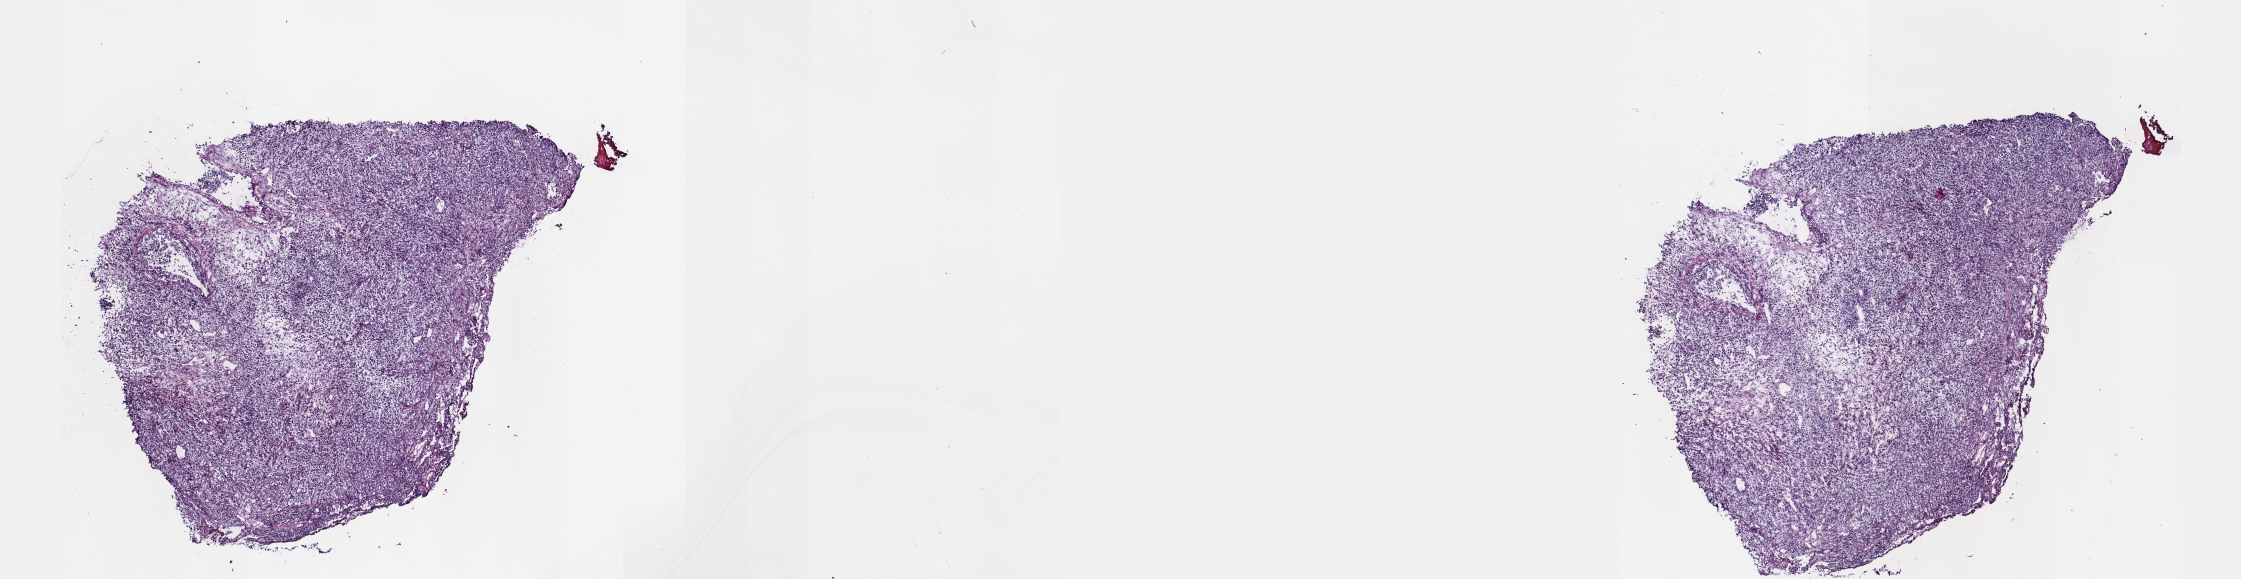
Hematoxylin and eosin (H&E) stained whole-slide image, a low-resolution overview of the entire scanned area, about 18.1 x 4.7 mm, frozen section from the top of the tissue portion, metastatic tumour sample, sampled site: upper lobe, lung. Male, age 75 years at initial diagnosis. Composition of this section per pathologist review: tumour cells 100%, tumour nuclei 80%, normal cells 0%, stromal cells 0%, necrosis 0%. Inflammatory infiltration, as recorded: lymphocyte infiltration 1%, monocyte infiltration 0%, neutrophil infiltration 0%.
* this section: metastatic tumour tissue
* patient diagnosis: Malignant melanoma, NOS